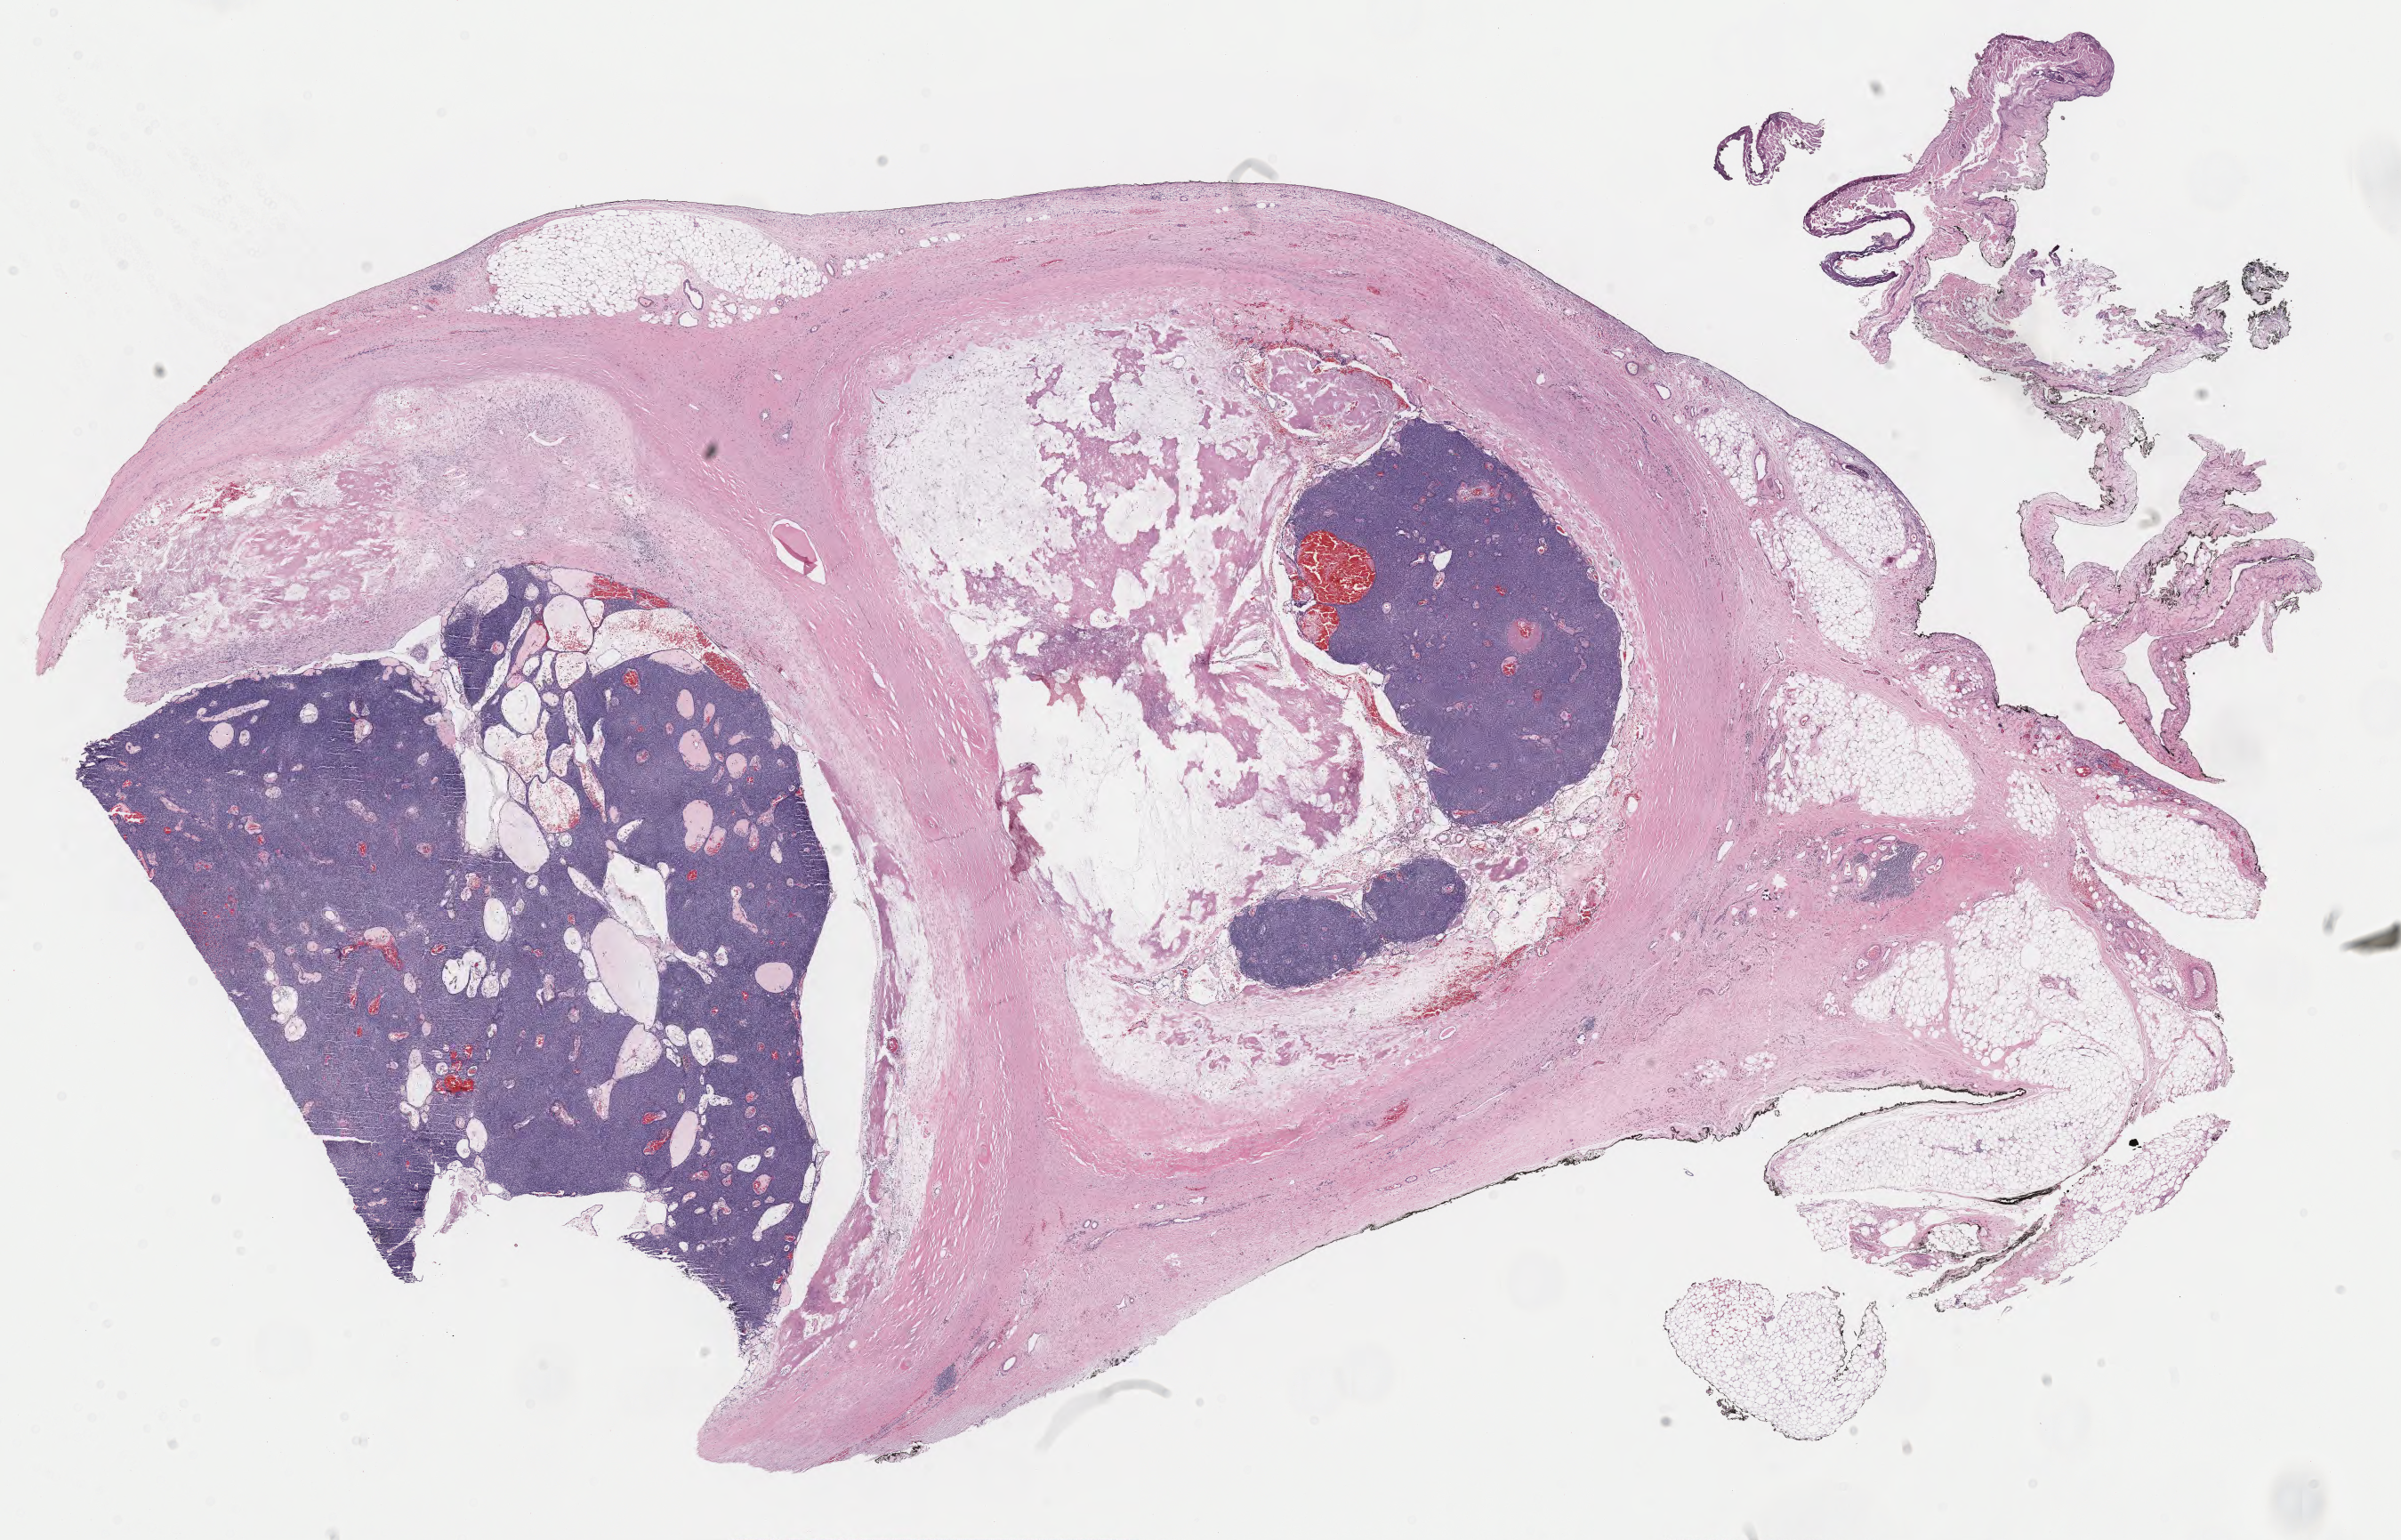
Whole-slide histology image, H&E — low-resolution overview of the scanned area, about 21.4 x 13.7 mm (from a 40x scan). Formalin-fixed paraffin-embedded (FFPE) diagnostic section. Thymus, primary tumour sample. Female patient; age at initial diagnosis 43 years.
Diagnosis: Thymoma, type B2, malignant.